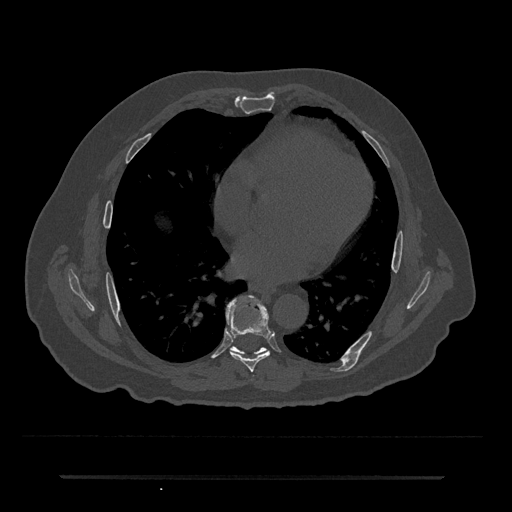
CT including the spine, one axial slice; slice 368 of 797 in the series (ordered by position); reconstruction kernel Br40s/3; 120 kVp; bone window (W 1800 / L 400 HU); 0.5 mm slice thickness; 512 × 512 image matrix, field of view 437 × 437 mm. Male patient, age 69 years. Case-level facts recorded for this patient, not image findings: primary cancer: prostate.
Annotated regions visible in this slice (semi-automatic segmentation, software-assisted and operator-edited):
- T7 vertebra: bounding box [x1, y1, x2, y2] px = [226, 295, 272, 372]
- T8 vertebra: [230, 346, 266, 355]